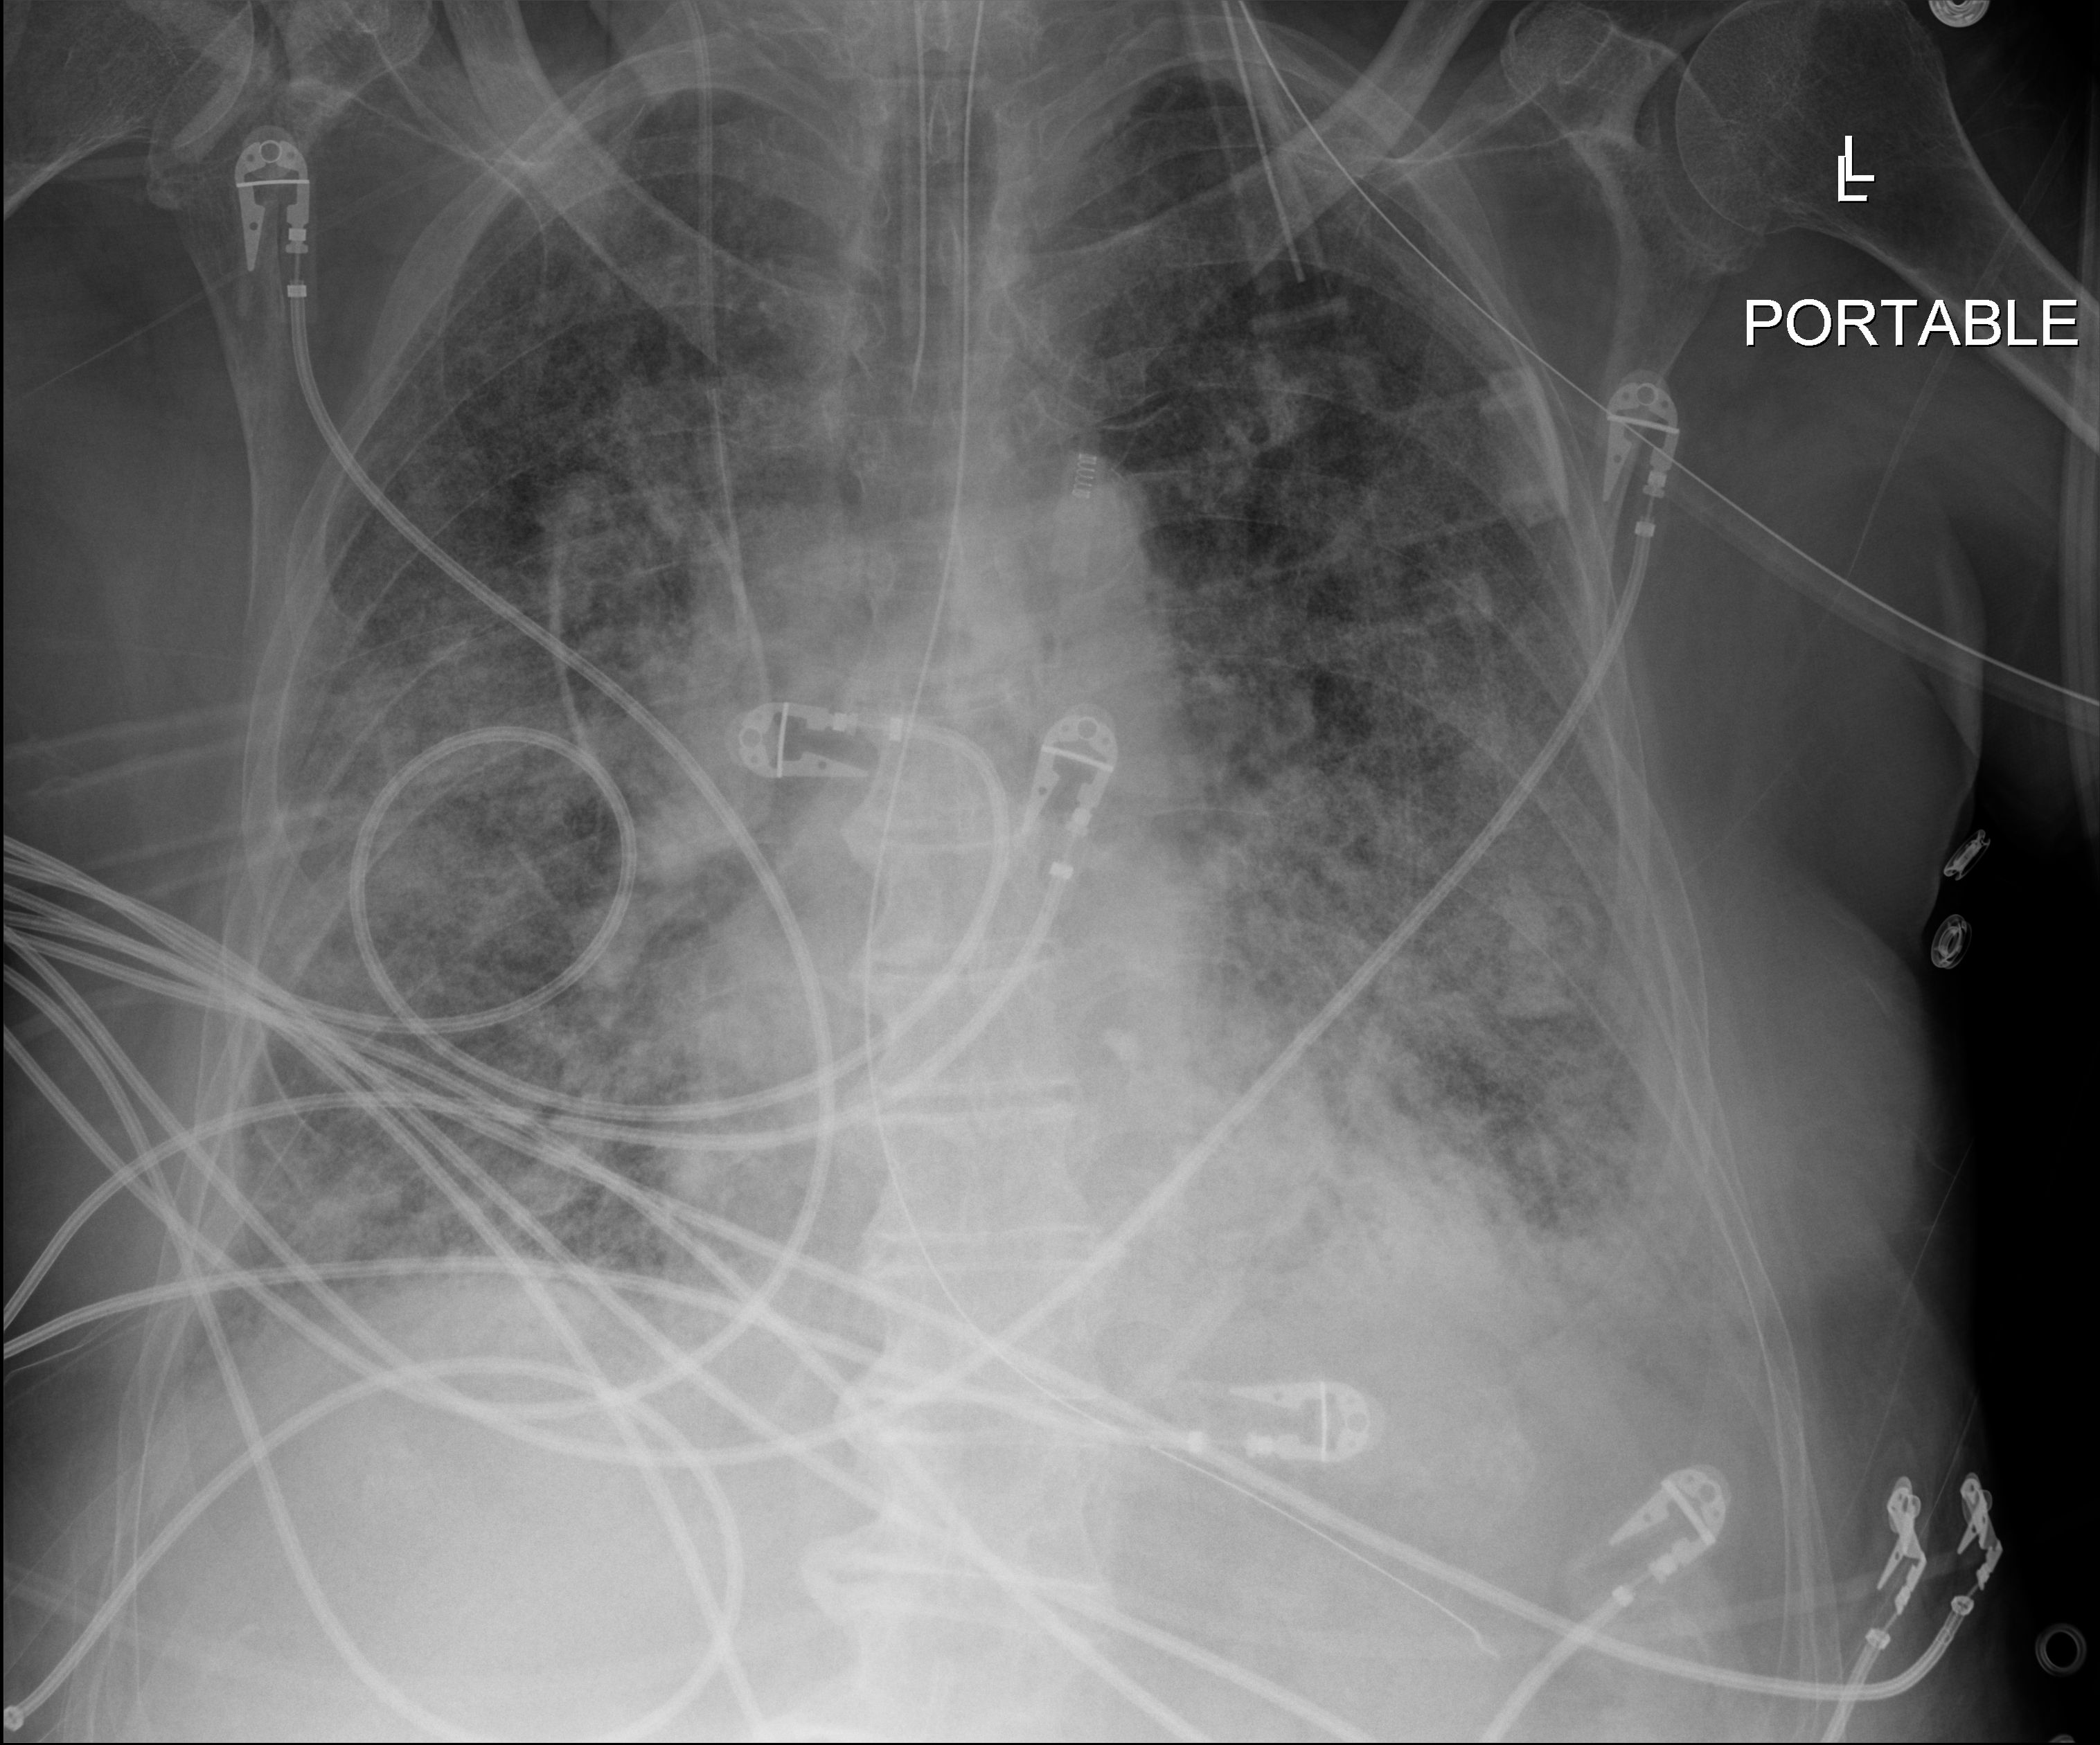
Chest X-ray (portable); anteroposterior (AP) projection. Patient hospitalised with COVID-19; male, aged 75–90 years.
Hospital-stay facts (about this admission, not read from this image; timing relative to this image not recorded): admitted to intensive care during this hospital stay: yes; mechanically ventilated during this hospital stay: yes.